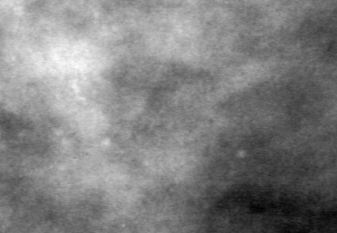
Cropped region of a digitized screen-film mammogram centred on a radiologist-marked abnormality, left breast, MLO view.
- Finding: calcifications, morphology pleomorphic, distribution clustered; BI-RADS assessment category 4; subtlety rating 1 on a 1 (subtle) to 5 (obvious) scale; pathology (as recorded): benign.